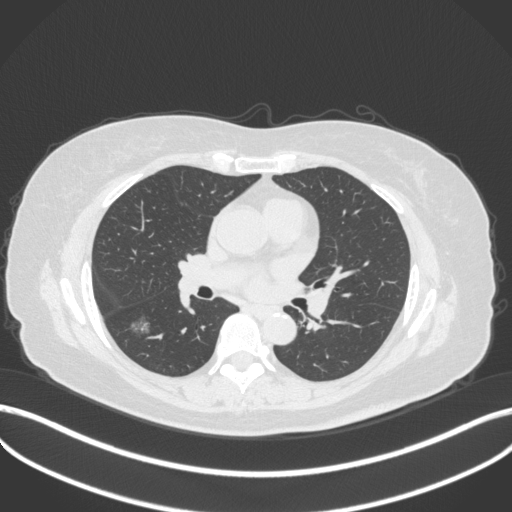
Chest CT, one axial slice; position 170 of 322 along the scan axis; reconstruction kernel B31f; 120 kVp; lung window (W 1500 / L -600 HU); 512 × 512 image matrix, field of view 400 × 400 mm. Patient: female, 64 years. Case-level facts recorded for this patient, not image findings: clinical TNM (as recorded): T1c N0 M0; histopathological grade: G1.
Structures marked on this image (bounding box drawn by a radiologist):
- lung tumour (recorded histology: adenocarcinoma): bounding box [x1, y1, x2, y2] px = [126, 309, 151, 336]